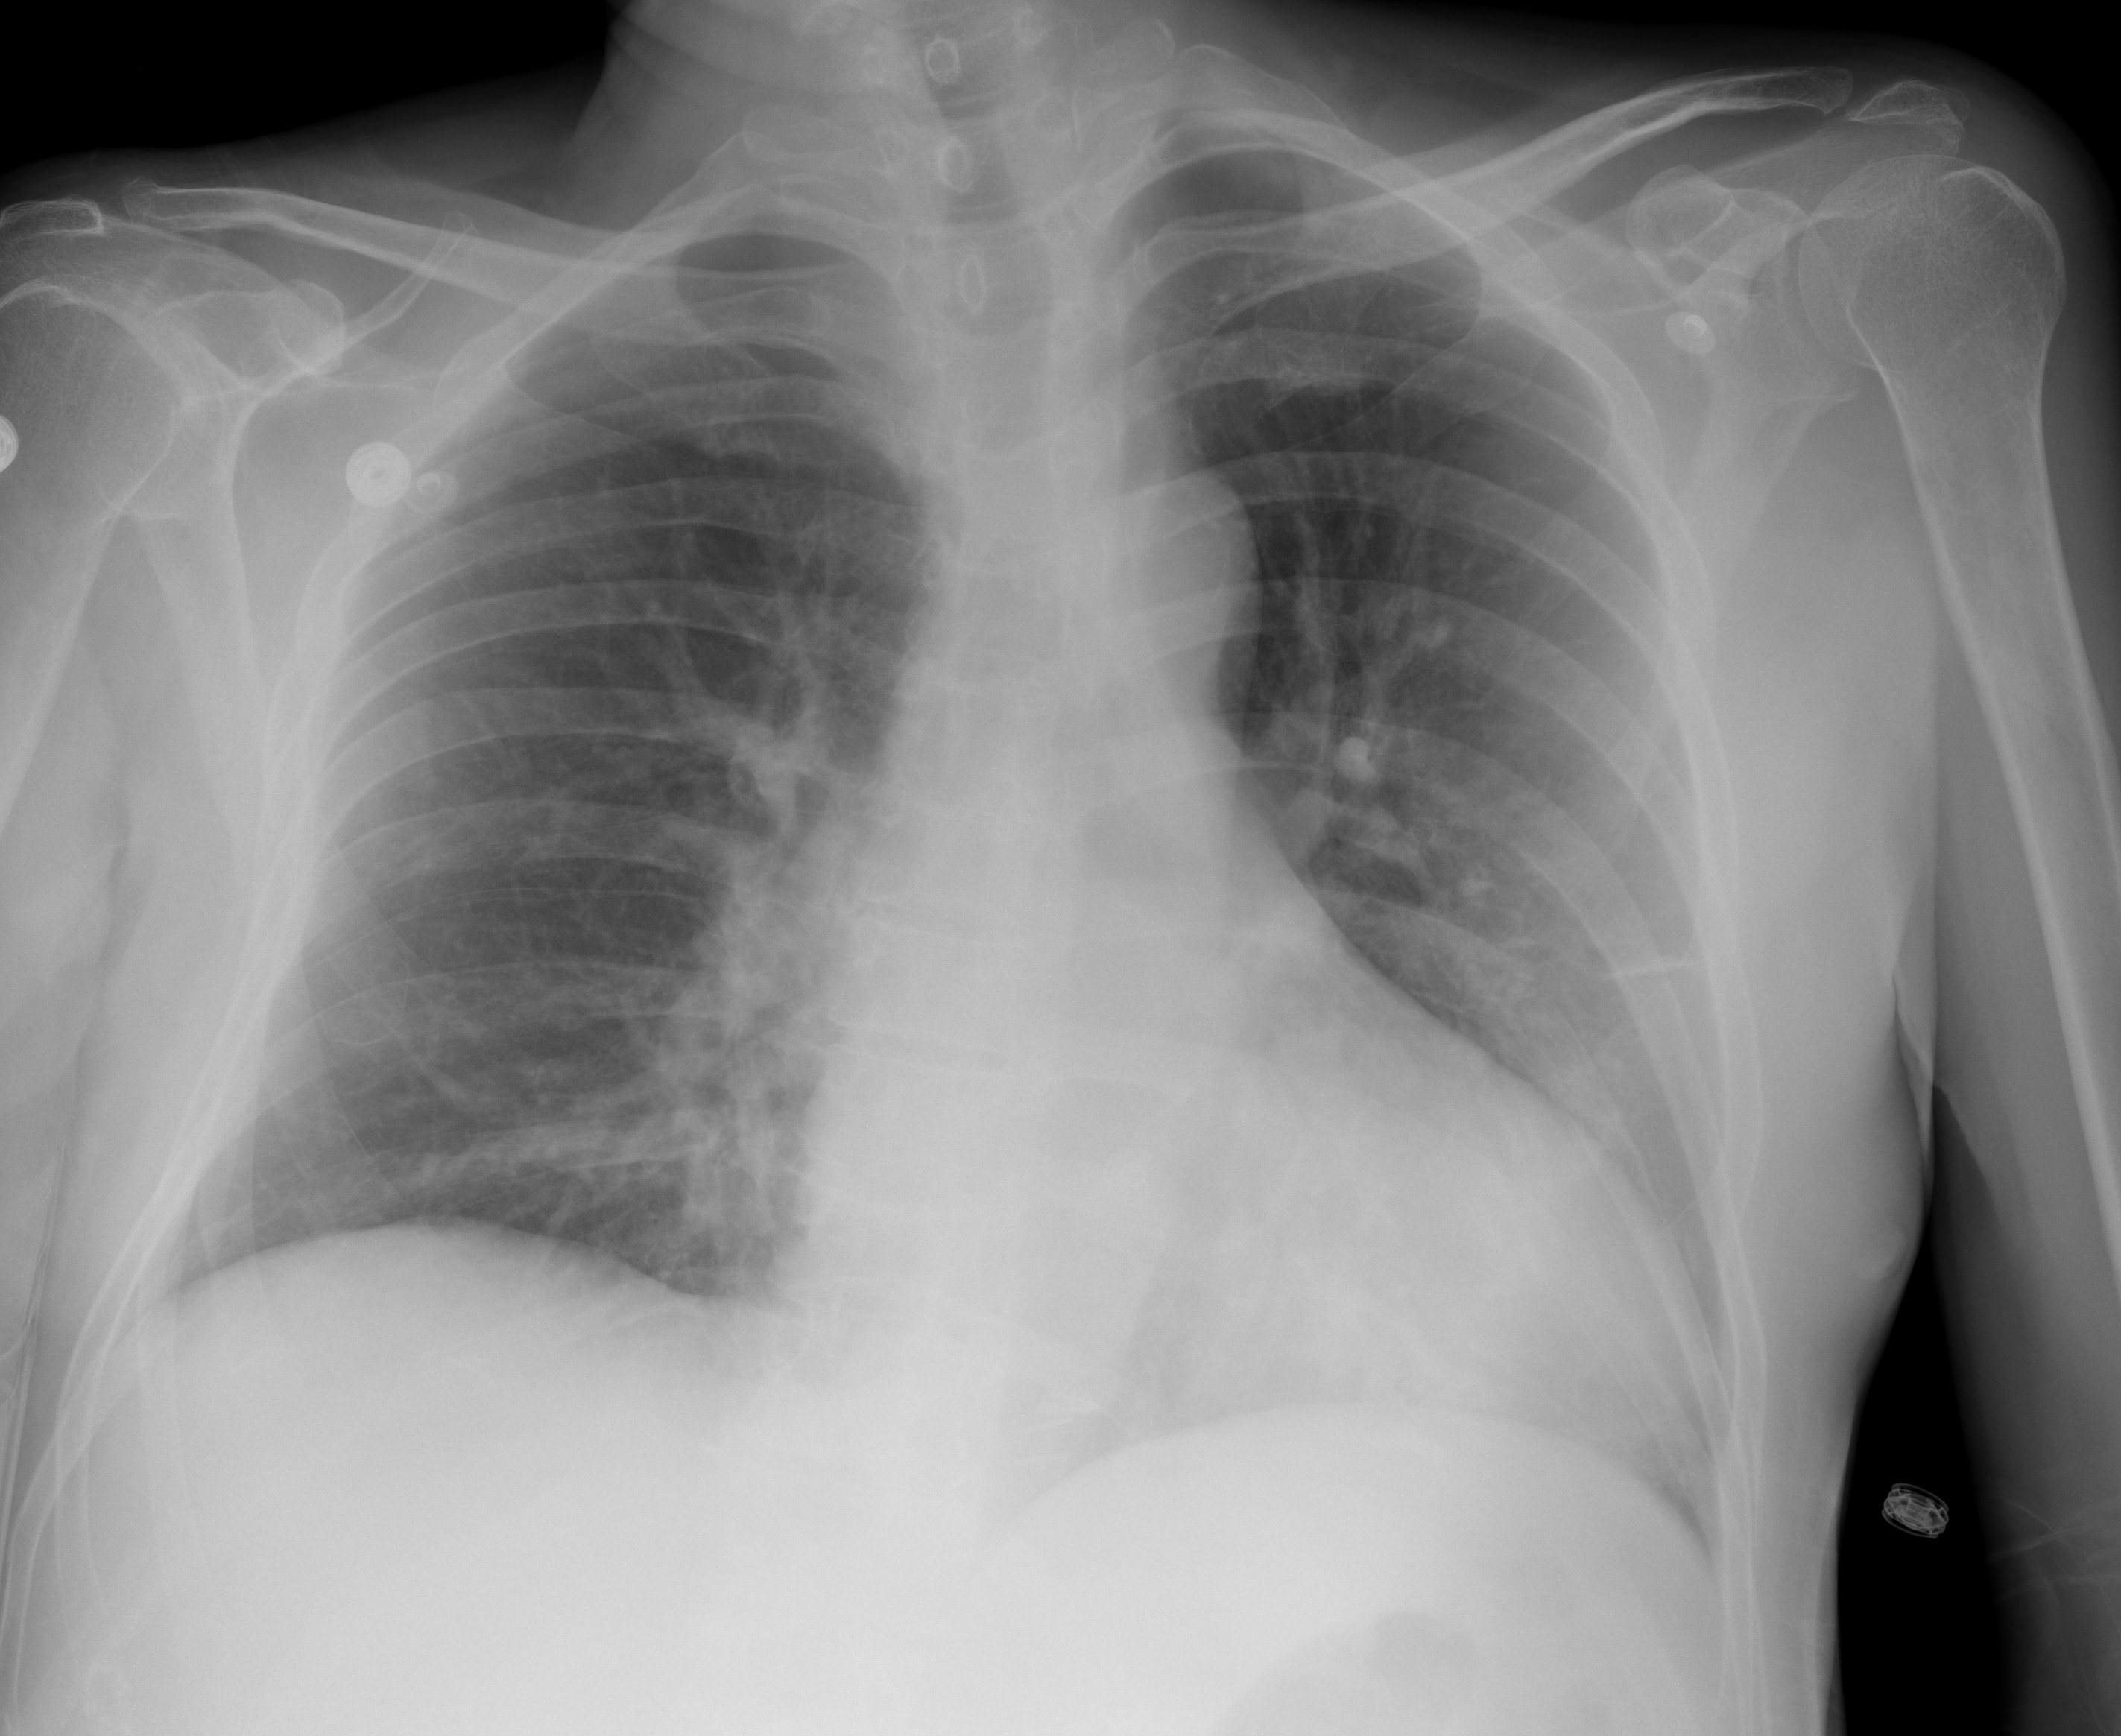
Chest X-ray (portable), AP projection. Male patient, age 61 years; COVID-19 (test-positive).
Key findings recorded by the radiologist: subtle airspace disease developing in the left lower lobe.